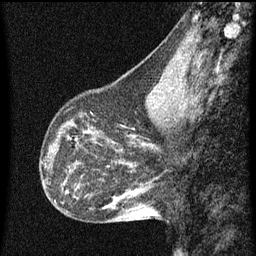
Breast MRI (dynamic contrast-enhanced), one sagittal slice. Slice 24 of 60 in the series (ordered by position). Dynamic contrast-enhanced series, image 2 of 3 at this slice position (ordered by acquisition). 1.5 T. TE 4.2 ms, TR 8 ms. 2 mm slice thickness. 256 × 256 image matrix, field of view 180 × 180 mm. Female patient, age 43 years.
Outlined on this slice (semi-automatic segmentation, software-assisted and operator-edited):
- analysis volume of interest (the breast-tissue region the enhancement analysis was run in; not a lesion): box from (x=53, y=104) to (x=101, y=151) px
- tumour enhancement mask (voxels above the 70 % enhancement threshold inside the analysis volume of interest): (x=68, y=136)–(x=70, y=139)